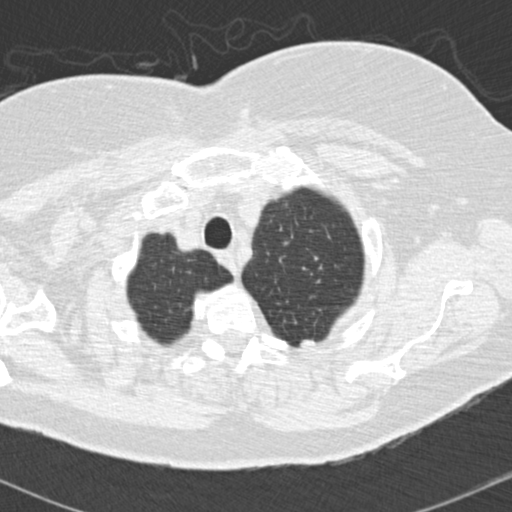
Low-dose screening chest CT, one axial slice; slice 146 of 174 in the series (ordered by position); 140 kVp; lung window (W 1500 / L -600 HU); 2 mm slice thickness; 512 × 512 image matrix, field of view 310 × 310 mm.
Annotated regions visible in this slice (expert manual segmentation):
- lesion 1 (tumor, upper lobe of left lung): bounding box (x1, y1, x2, y2) in pixels: (300, 339, 314, 349)